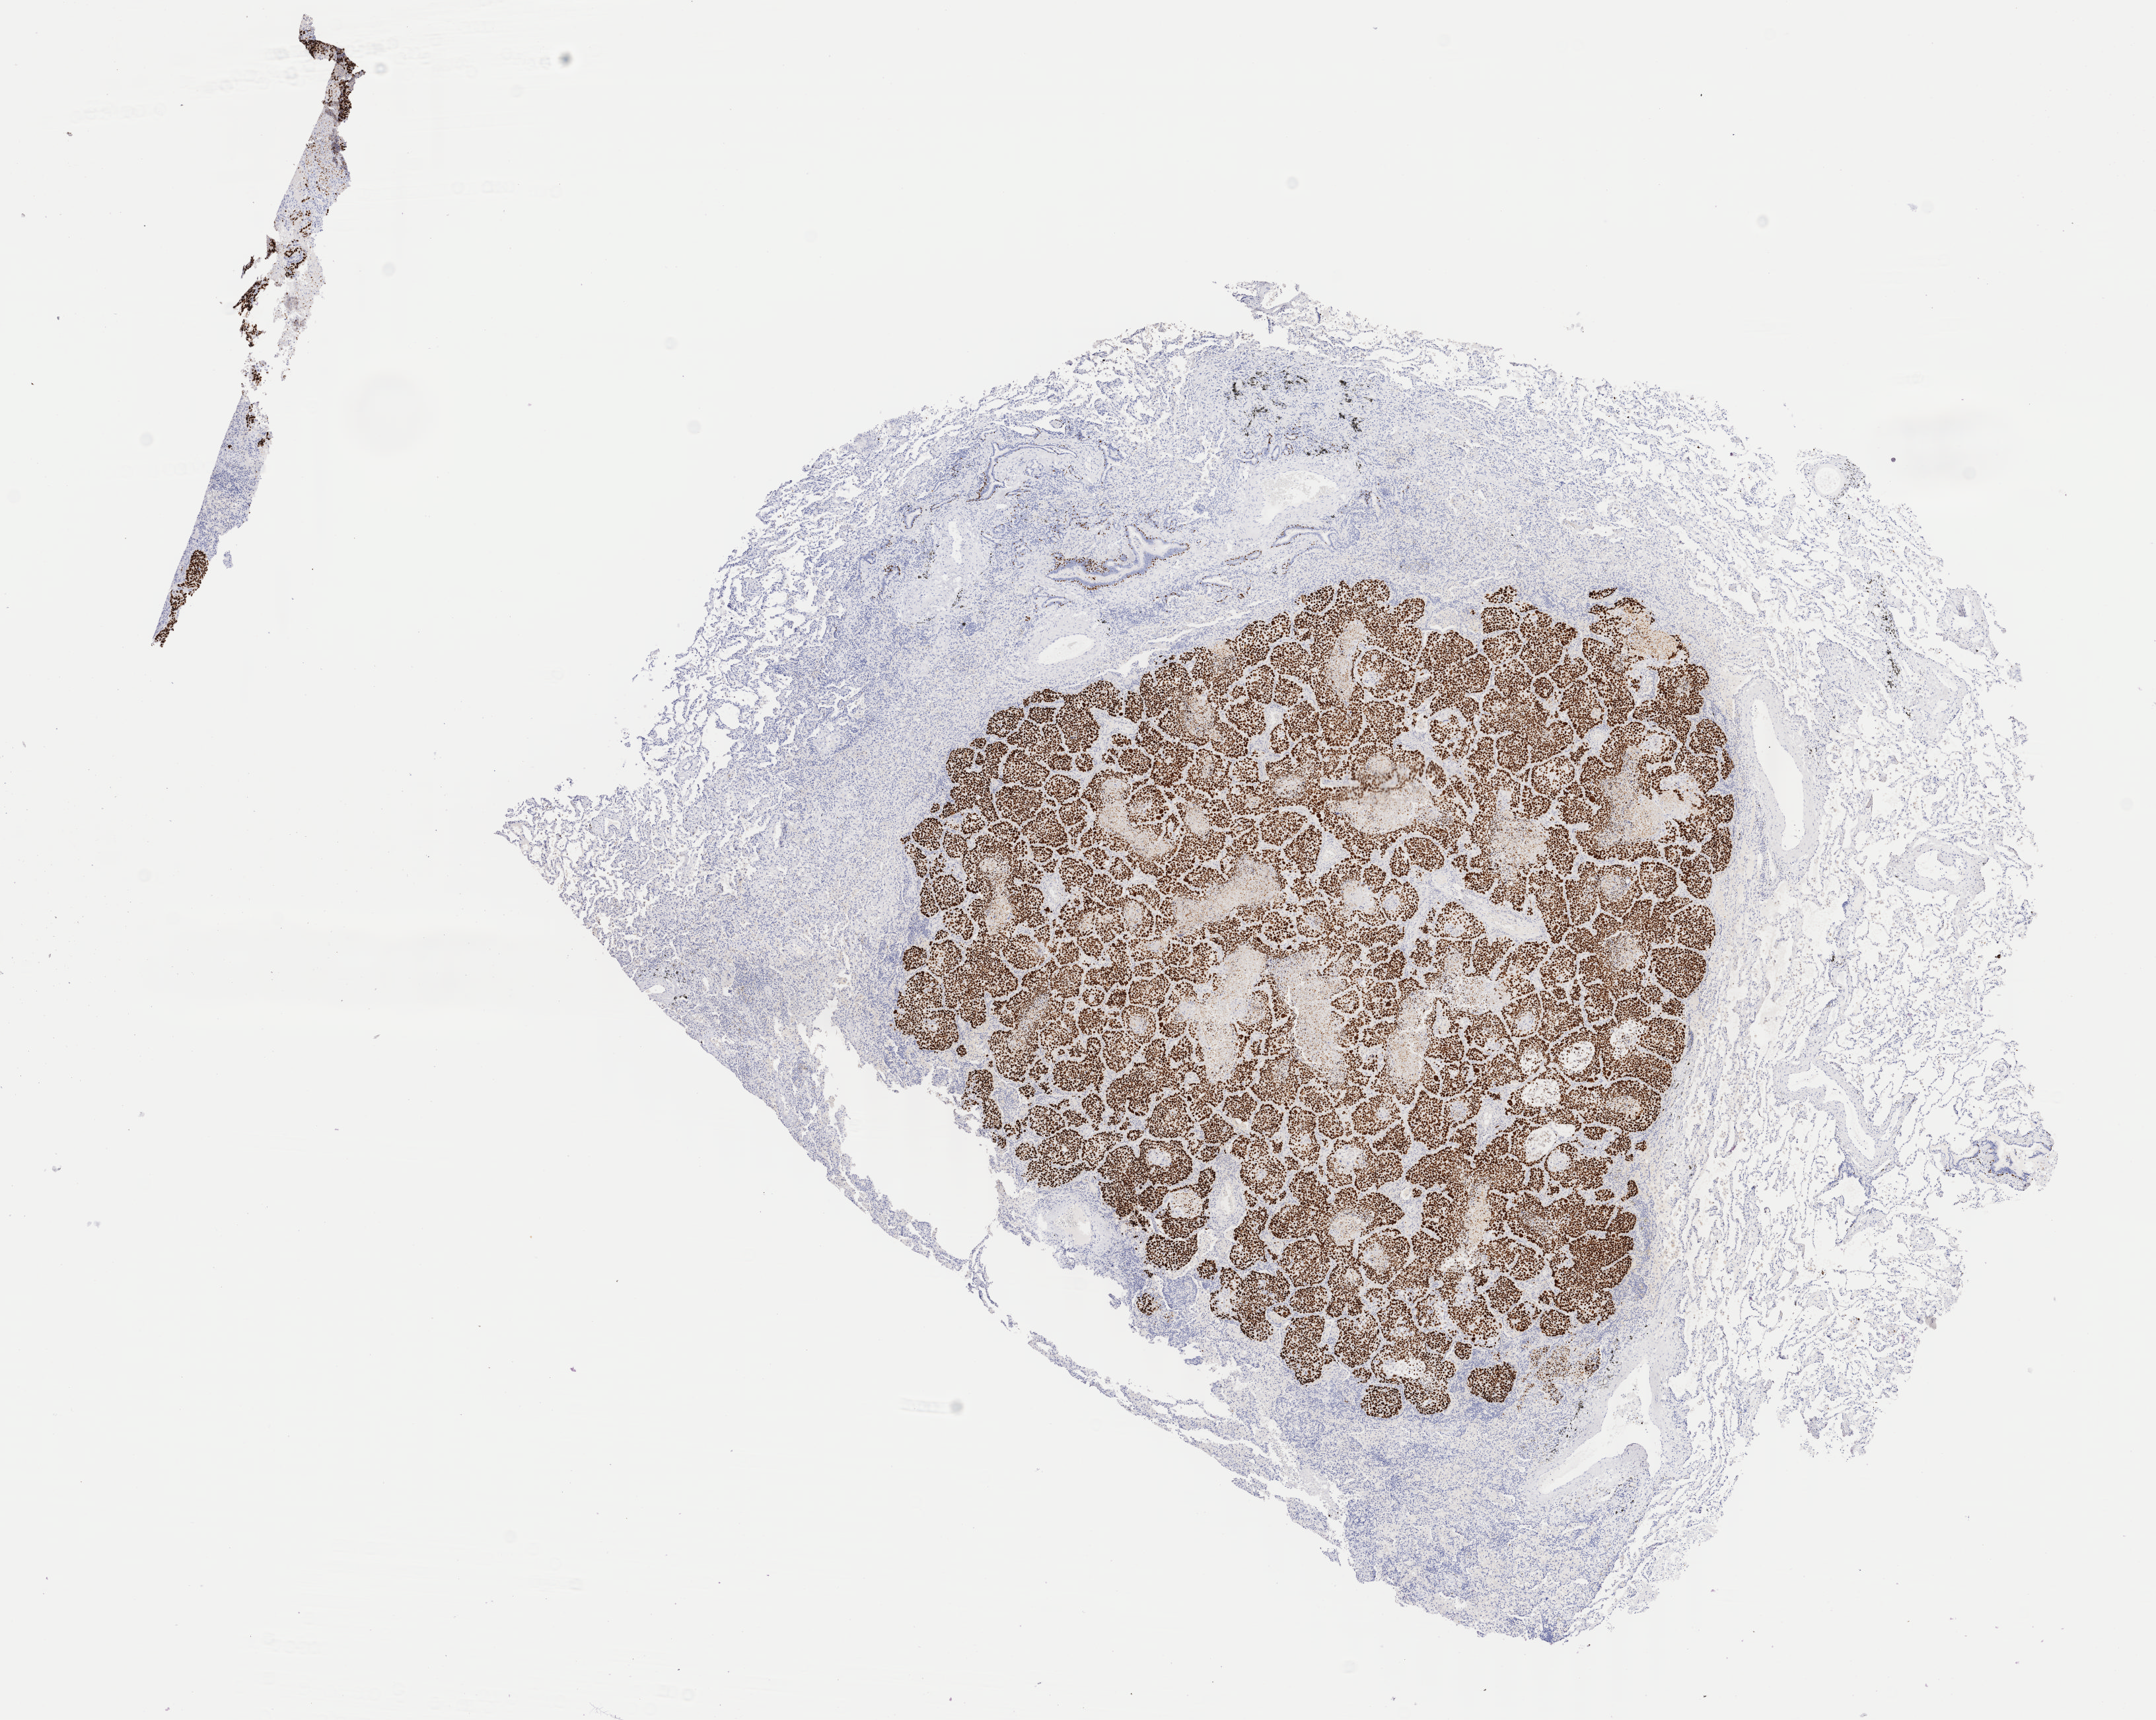
Whole-slide image, immunohistochemical stain for p40, a low-resolution overview of the entire scanned area, about 13.0 x 10.4 mm. Specimen: tumor tissue. Anatomic site: lung (left). Patient male; 66 years old.
- diagnosis: Squamous cell carcinoma, NOS